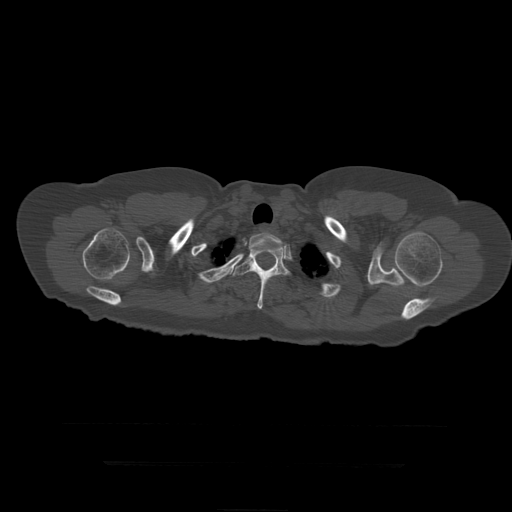
CT including the spine, one axial slice; slice 366 of 399 in the series (ordered by position); reconstruction kernel STANDARD; 120 kVp; bone window (W 1800 / L 400 HU); 1.25 mm slice thickness; 512 × 512 image matrix. Patient age 41 years. Case-level facts recorded for this patient, not image findings: primary cancer: breast.
Outlined on this slice (semi-automatically segmented with operator editing):
- T2 vertebra: box from (x=243, y=233) to (x=284, y=271) px
- T3 vertebra: (x=231, y=248)–(x=291, y=309)